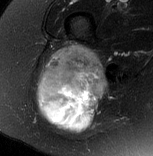
MRI of an extremity soft-tissue mass, one axial slice. Position 47 of 77 along the scan axis. T2-weighted fat-saturated. MR volume resampled by the dataset authors to the PET/CT grid (not the native acquisition matrix). 153 × 156 image matrix. Female patient. From the clinical record (not read from this slice): histological type: synovial sarcoma; grade: intermediate; site of the primary tumour: right buttock.
Outlined on this slice (expert contour drawn on MRI and transferred to this co-registered scan by the dataset authors):
- gross tumour volume including surrounding oedema: bounding box [x1, y1, x2, y2] px = [37, 45, 107, 133]
- gross tumour volume (mass): [37, 45, 107, 126]